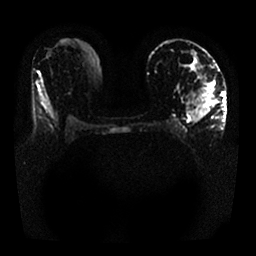
Breast MRI, one axial slice. Slice 13 of 25 in the series (ordered by position). Diffusion-weighted series; image 2 of 4 stored at this slice position (different b-values; order by instance number). 1.5 T. 4 mm slice thickness. 256 × 256 image matrix. Female patient.
Outlined on this slice (outlined manually by an expert reader):
- tumour on diffusion-weighted imaging: box from (x=192, y=81) to (x=215, y=119) px